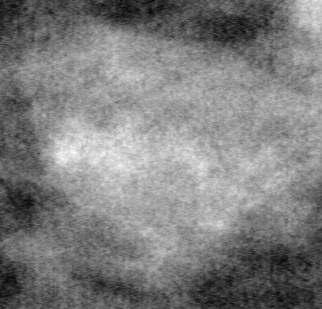
Crop from a digitized film mammogram around one marked abnormality; left breast; CC view.
- Finding: mass, shape lobulated, margins ill defined; BI-RADS assessment category 4; pathology result (as recorded, not read from the image): benign.